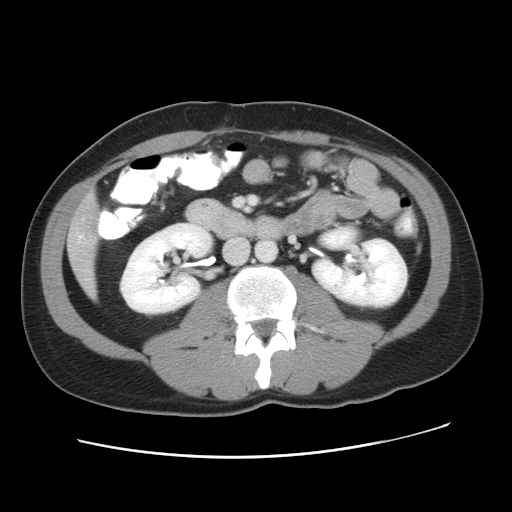
Contrast-enhanced abdominal CT, one axial slice; position 16 of 49 along the scan axis; intravenous contrast given; soft-tissue window (W 400 / L 40 HU); 5 mm slice thickness; 512 × 512 image matrix, field of view 363 × 363 mm. Male patient, age 41 years. Case-level facts recorded for this patient, not image findings: diagnosis: colorectal cancer liver metastases, imaged before liver resection; multiple liver metastases: yes; largest metastasis: 0.7 cm; disease in both lobes: yes.
Outlined on this slice (outlined manually by an expert reader):
- hepatic veins: bounding box [x1, y1, x2, y2] px = [79, 235, 83, 239]
- liver: [68, 195, 98, 294]